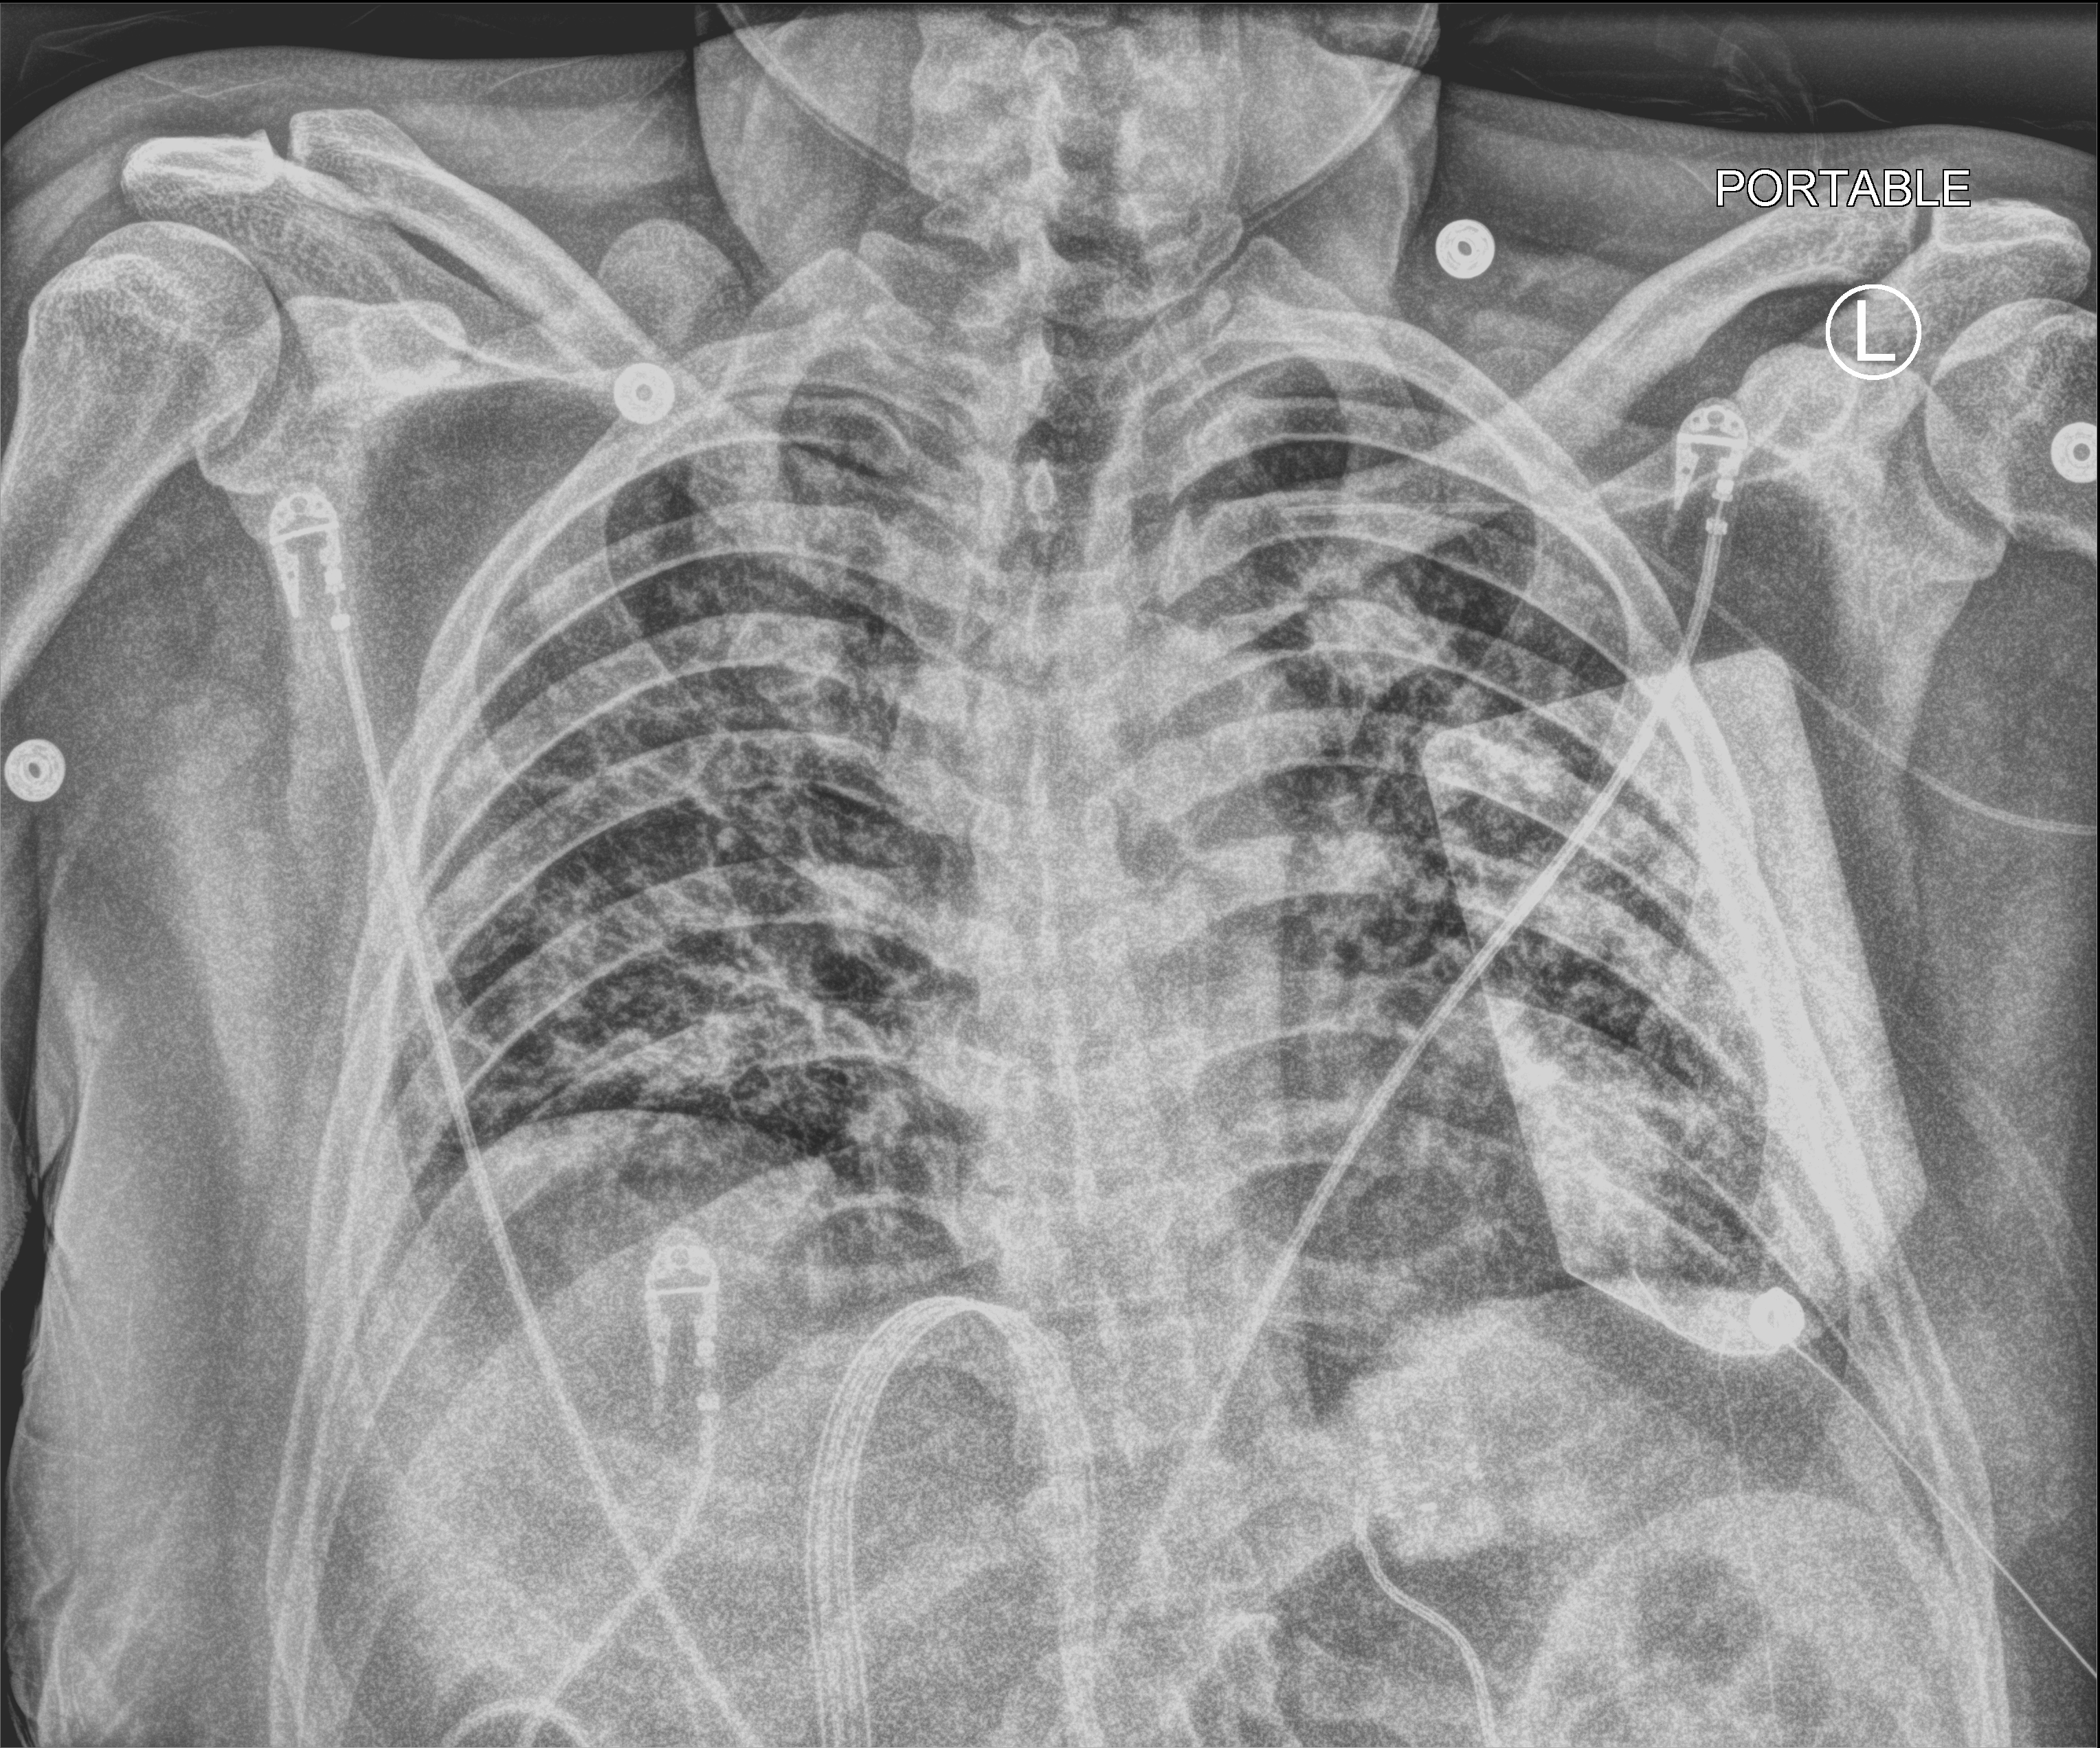
Chest X-ray (portable), anteroposterior (AP) projection. Male patient hospitalised with COVID-19, age 18–59 years.
Admission-level facts for this patient (not findings on this image; timing relative to this image not recorded):
- admitted to intensive care during this hospital stay: yes
- length of hospital stay: 29 days
- mechanically ventilated during this hospital stay: yes